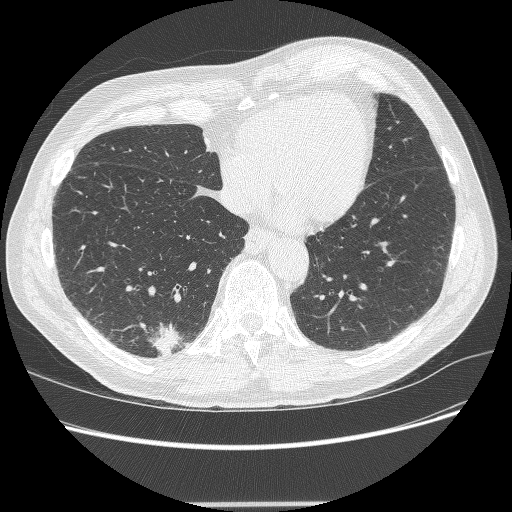
Chest CT (low-dose screening protocol), one axial image; second annual screen; lung window (W 1500 / L -600 HU); 1.25 mm slice thickness; lung (sharp) reconstruction kernel (BONE); slice 73 of 245 in the series. Male, age 71 years at enrolment. Current smoker at enrolment.
Expert reader's lesion annotation, bounding box [x1, y1, x2, y2] px = [137, 323, 189, 364]. The screening reader recorded 5 non-calcified nodules or masses ≥4 mm on this exam (right lower lobe, right lower lobe, right upper lobe, right upper lobe, right upper lobe); which of them this box marks is not recorded.